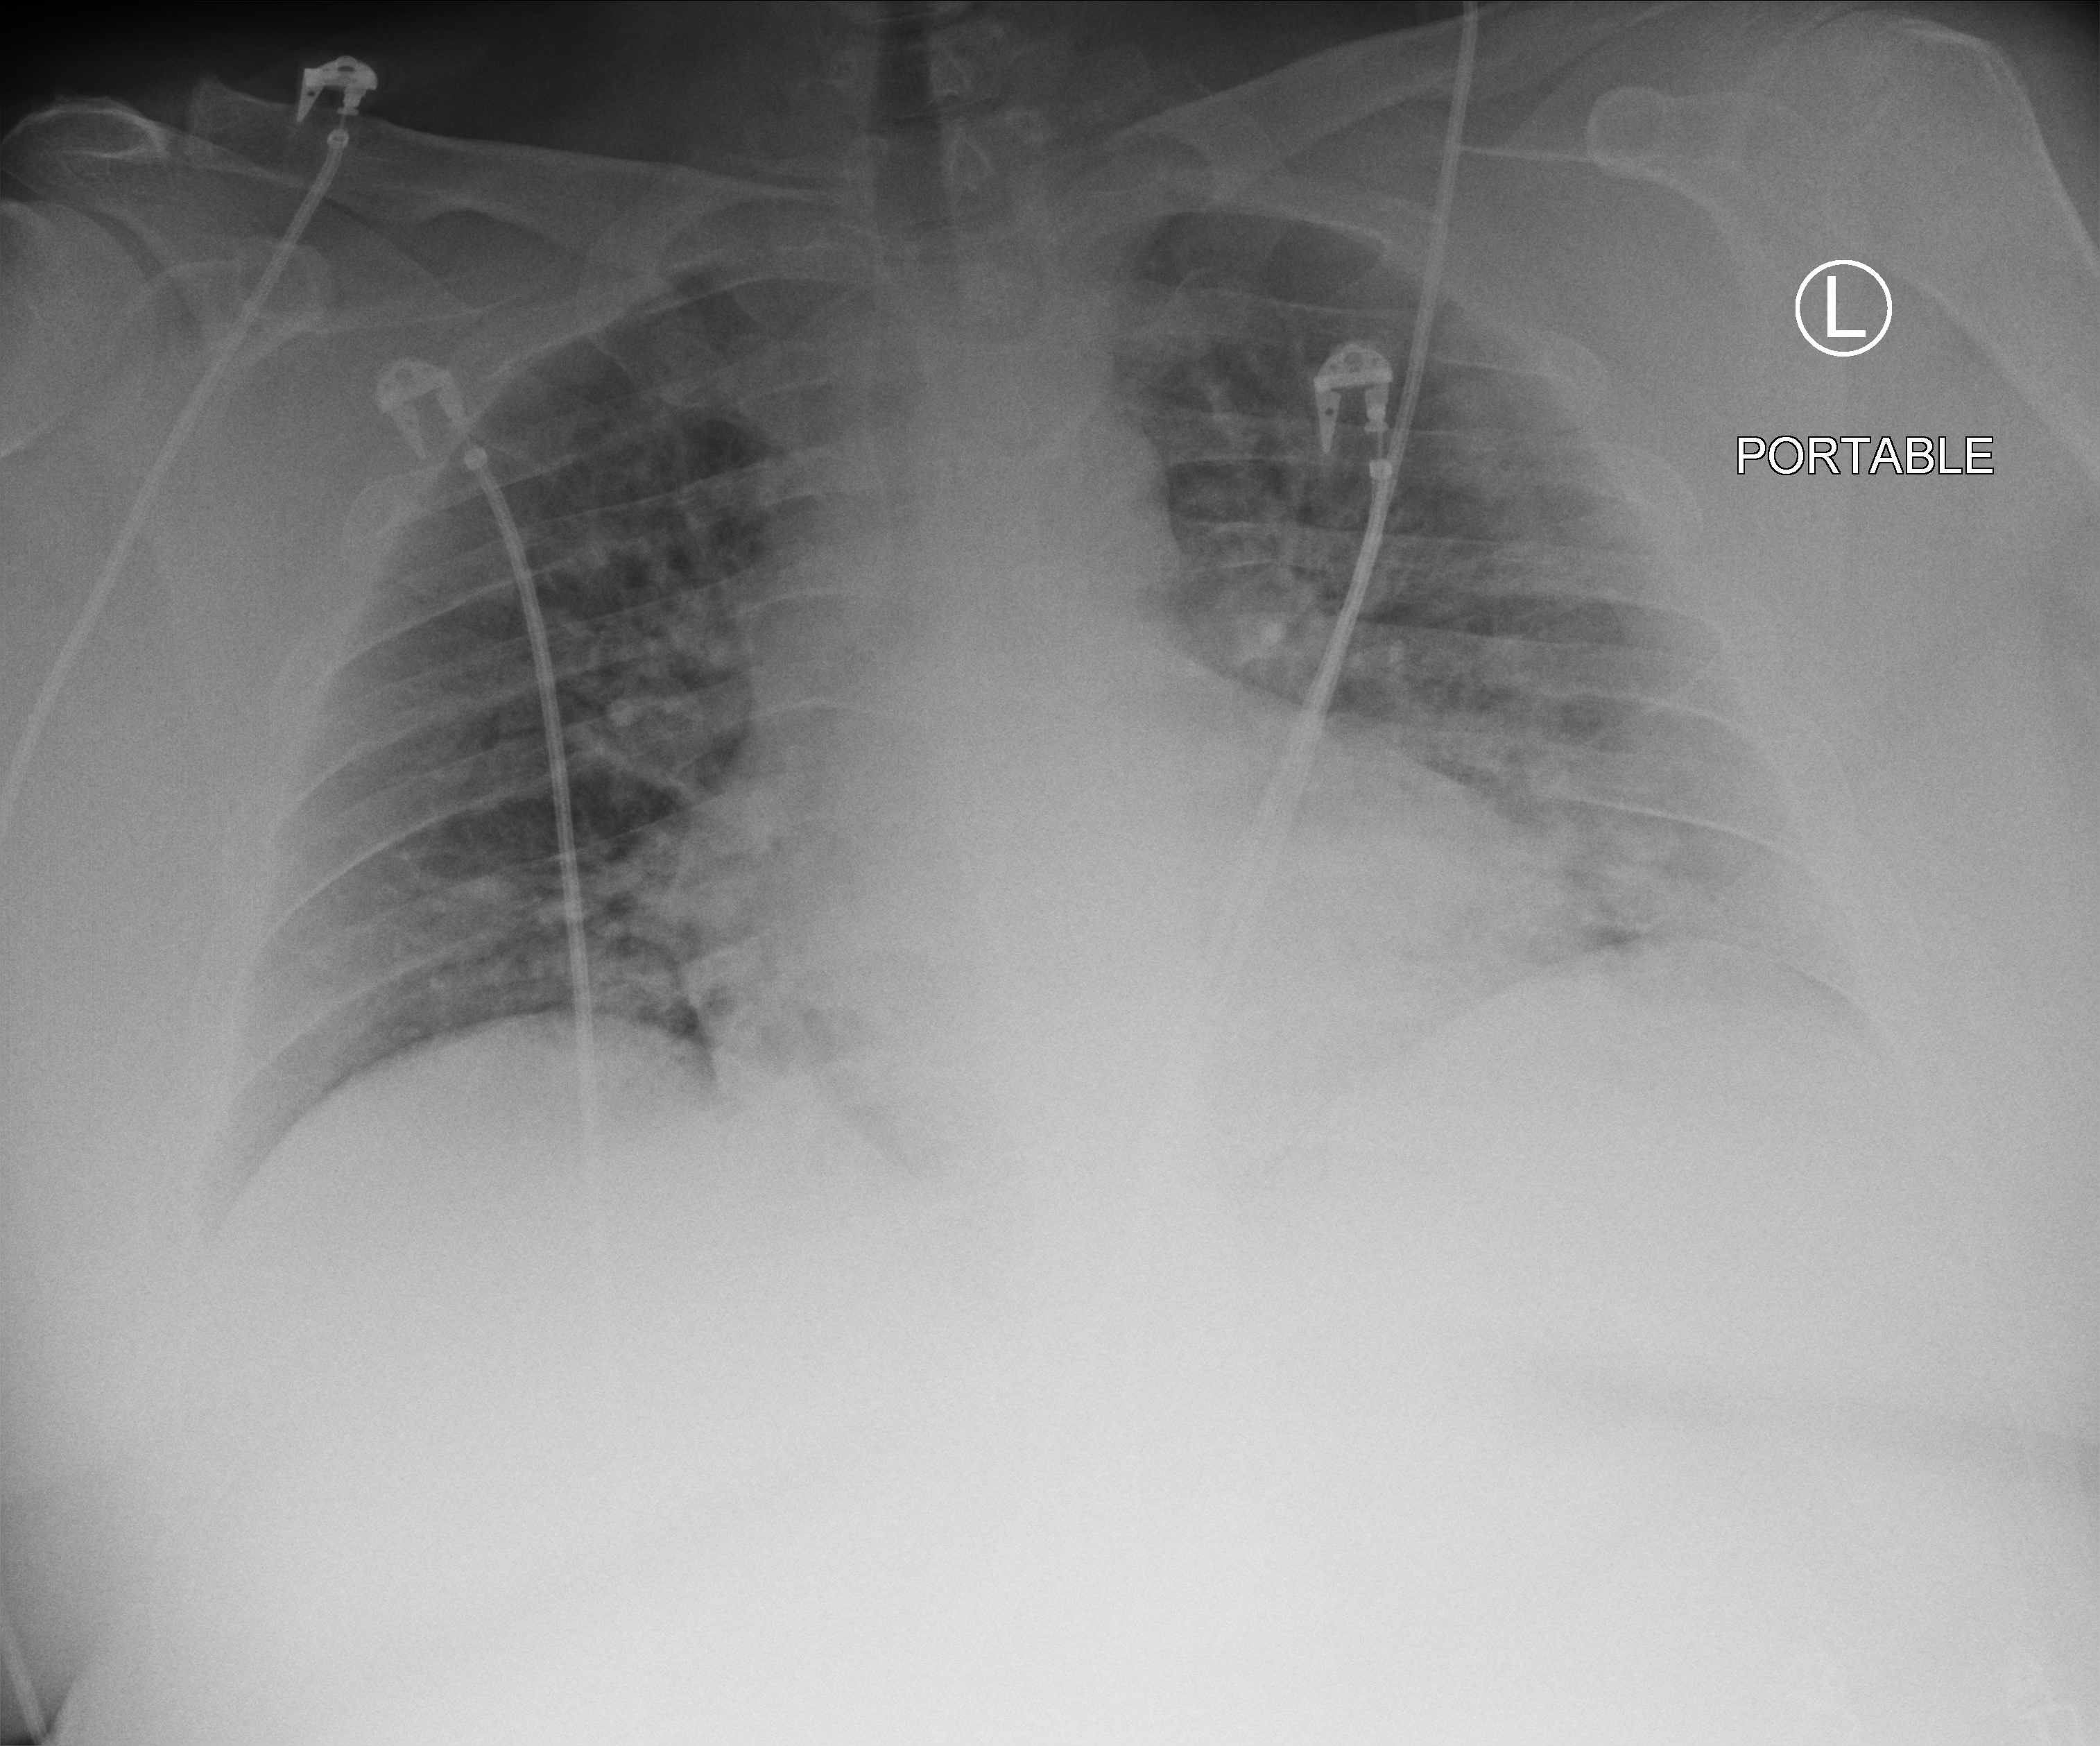
Bedside chest radiograph (computed radiography). Patient hospitalised with COVID-19; male, aged 18–59 years.
Hospital-stay facts (about this admission, not read from this image; timing relative to this image not recorded): mechanically ventilated during this hospital stay: no; admitted to intensive care during this hospital stay: no.